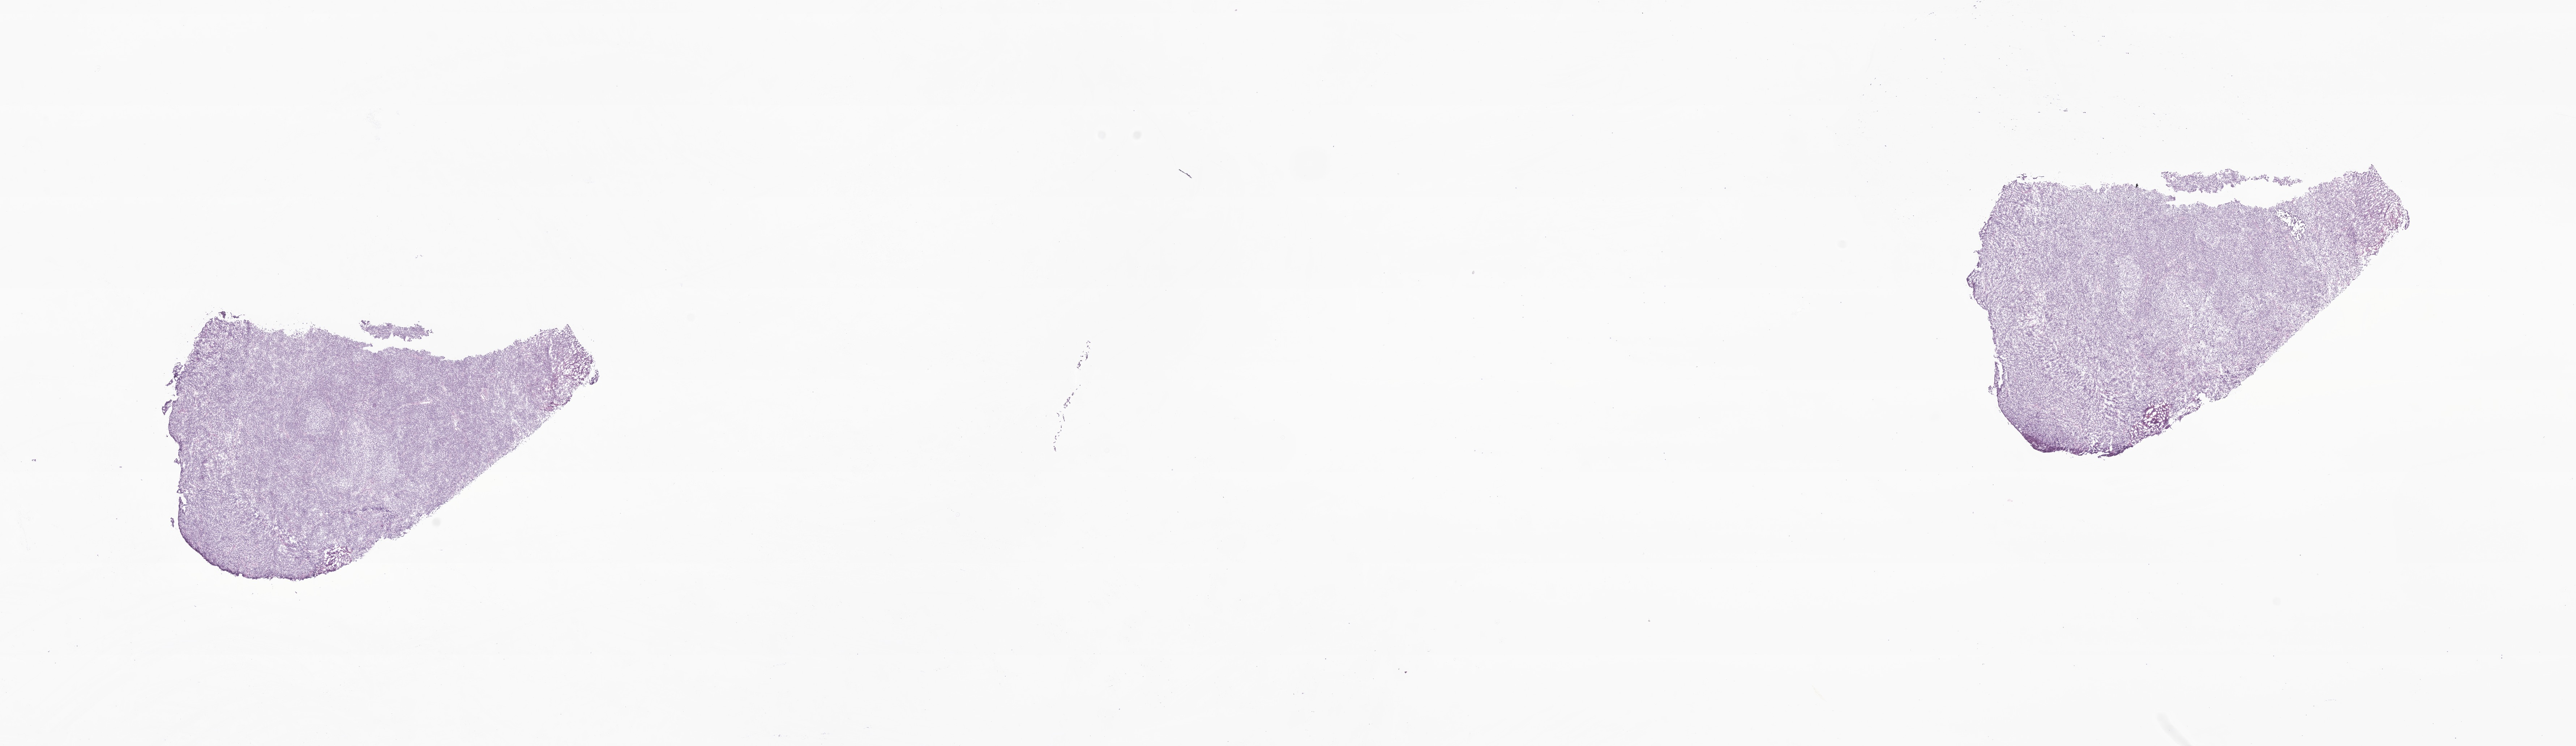
Whole-slide image, hematoxylin and eosin (H&E) stain of tumor tissue from the brain, a low-resolution overview of the entire scanned area, about 30.0 x 8.7 mm. Cryosection (OCT / tissue freezing medium). Patient: female, age 766 days (about 2.1 years).
Recorded diagnosis: Desmoplastic nodular medulloblastoma.